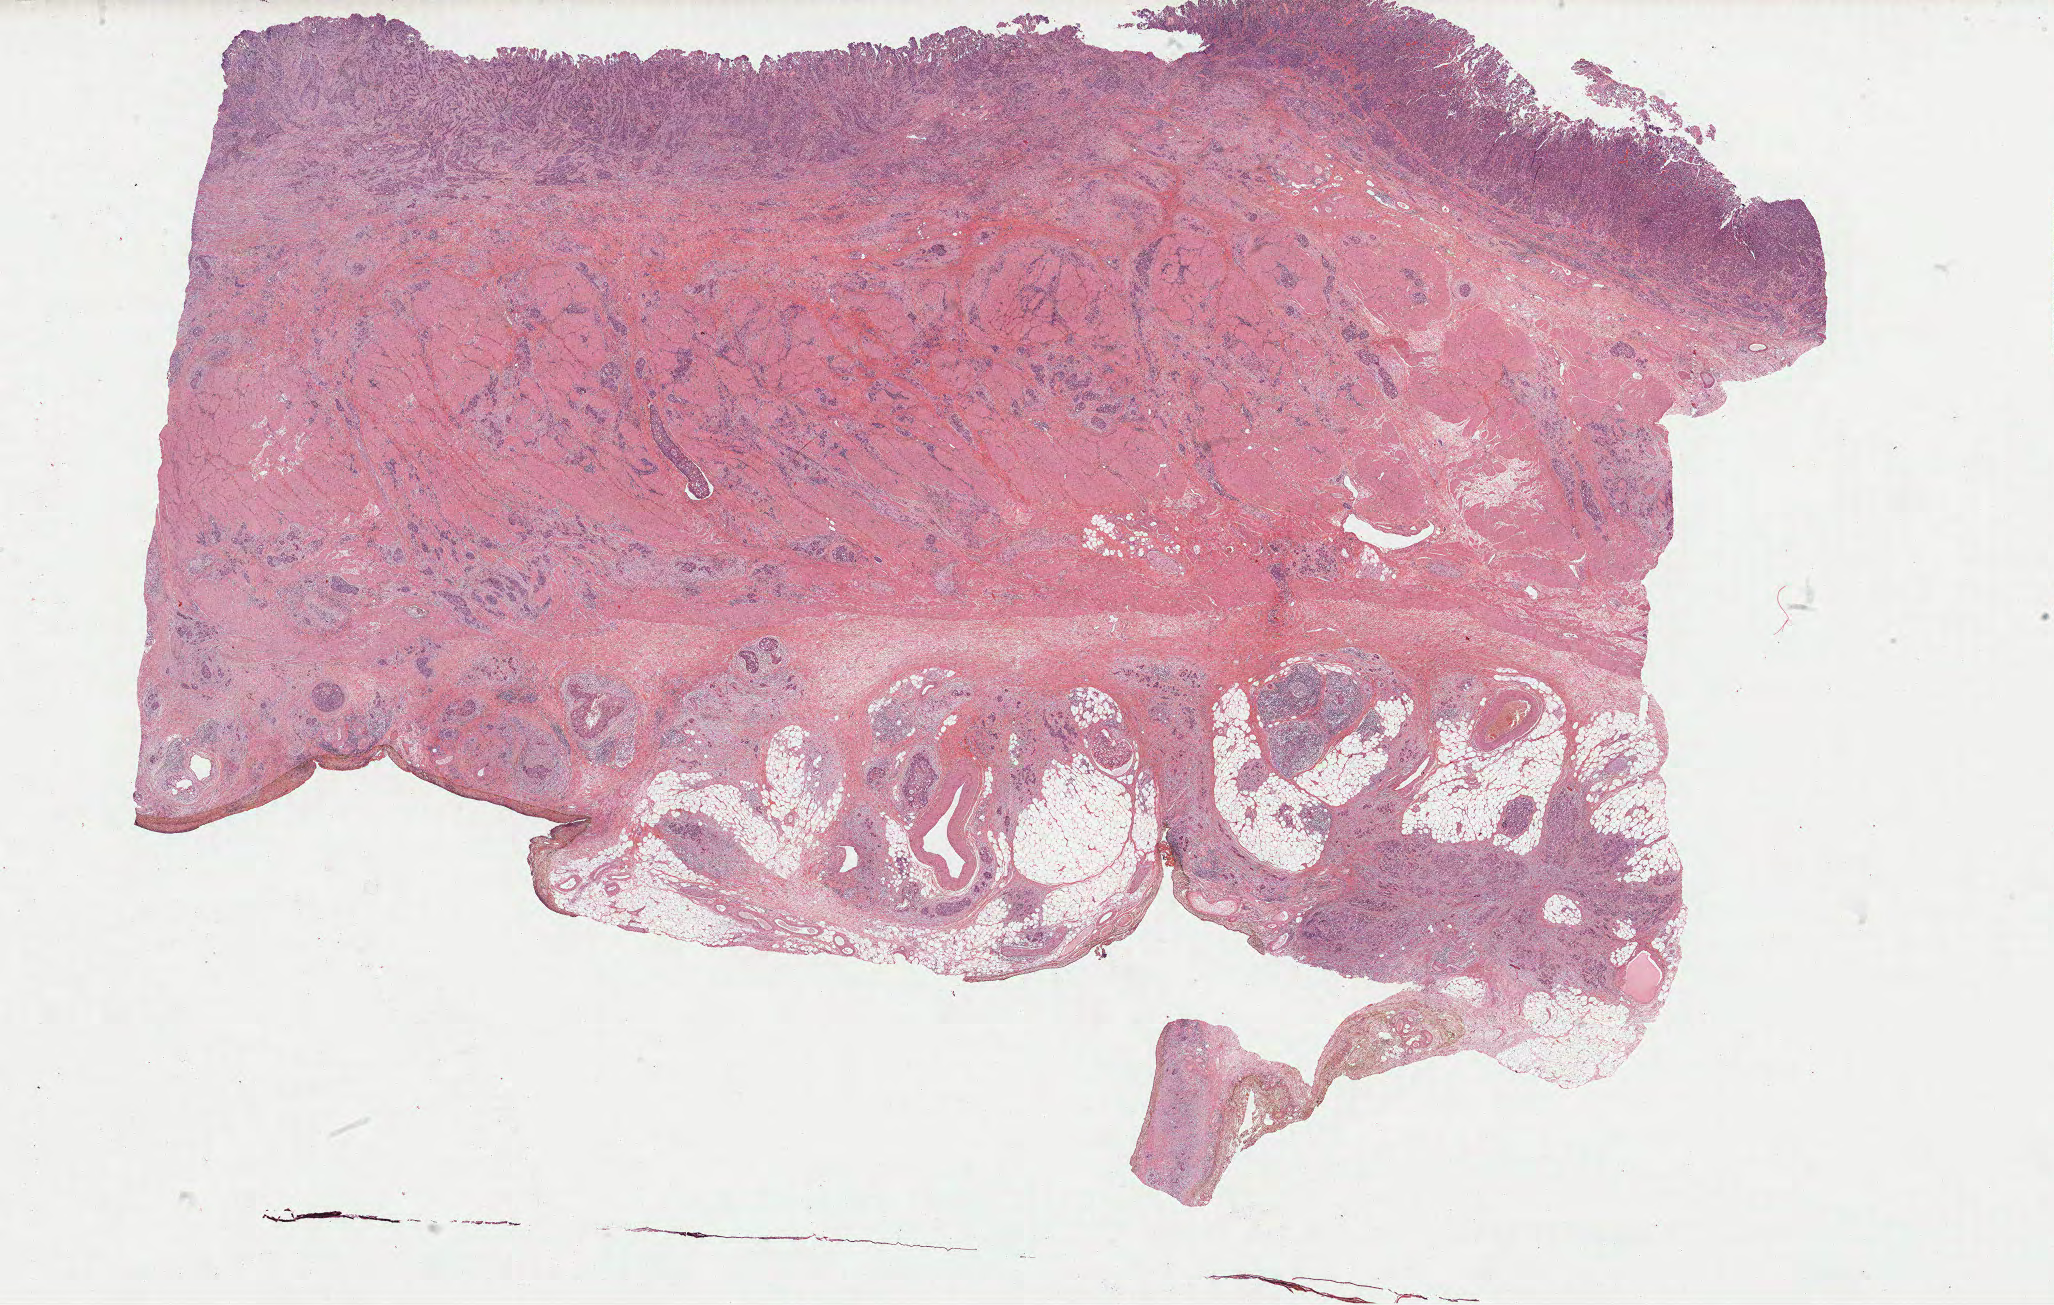
Digitized H&E-stained tissue section (whole slide) — shown as a low-resolution overview of the whole scanned area (about 33.0 x 21.0 mm); formalin-fixed paraffin-embedded (FFPE) diagnostic section; primary tumour sample from the stomach. Patient: male, age at initial diagnosis 66 years. Histologic grade: G3 (poorly differentiated).
- lymph nodes positive (case pathology): 55 of 56 examined
- diagnosis: Adenocarcinoma, intestinal type (fundus of stomach)
- AJCC pathologic stage: IV (6th edition)